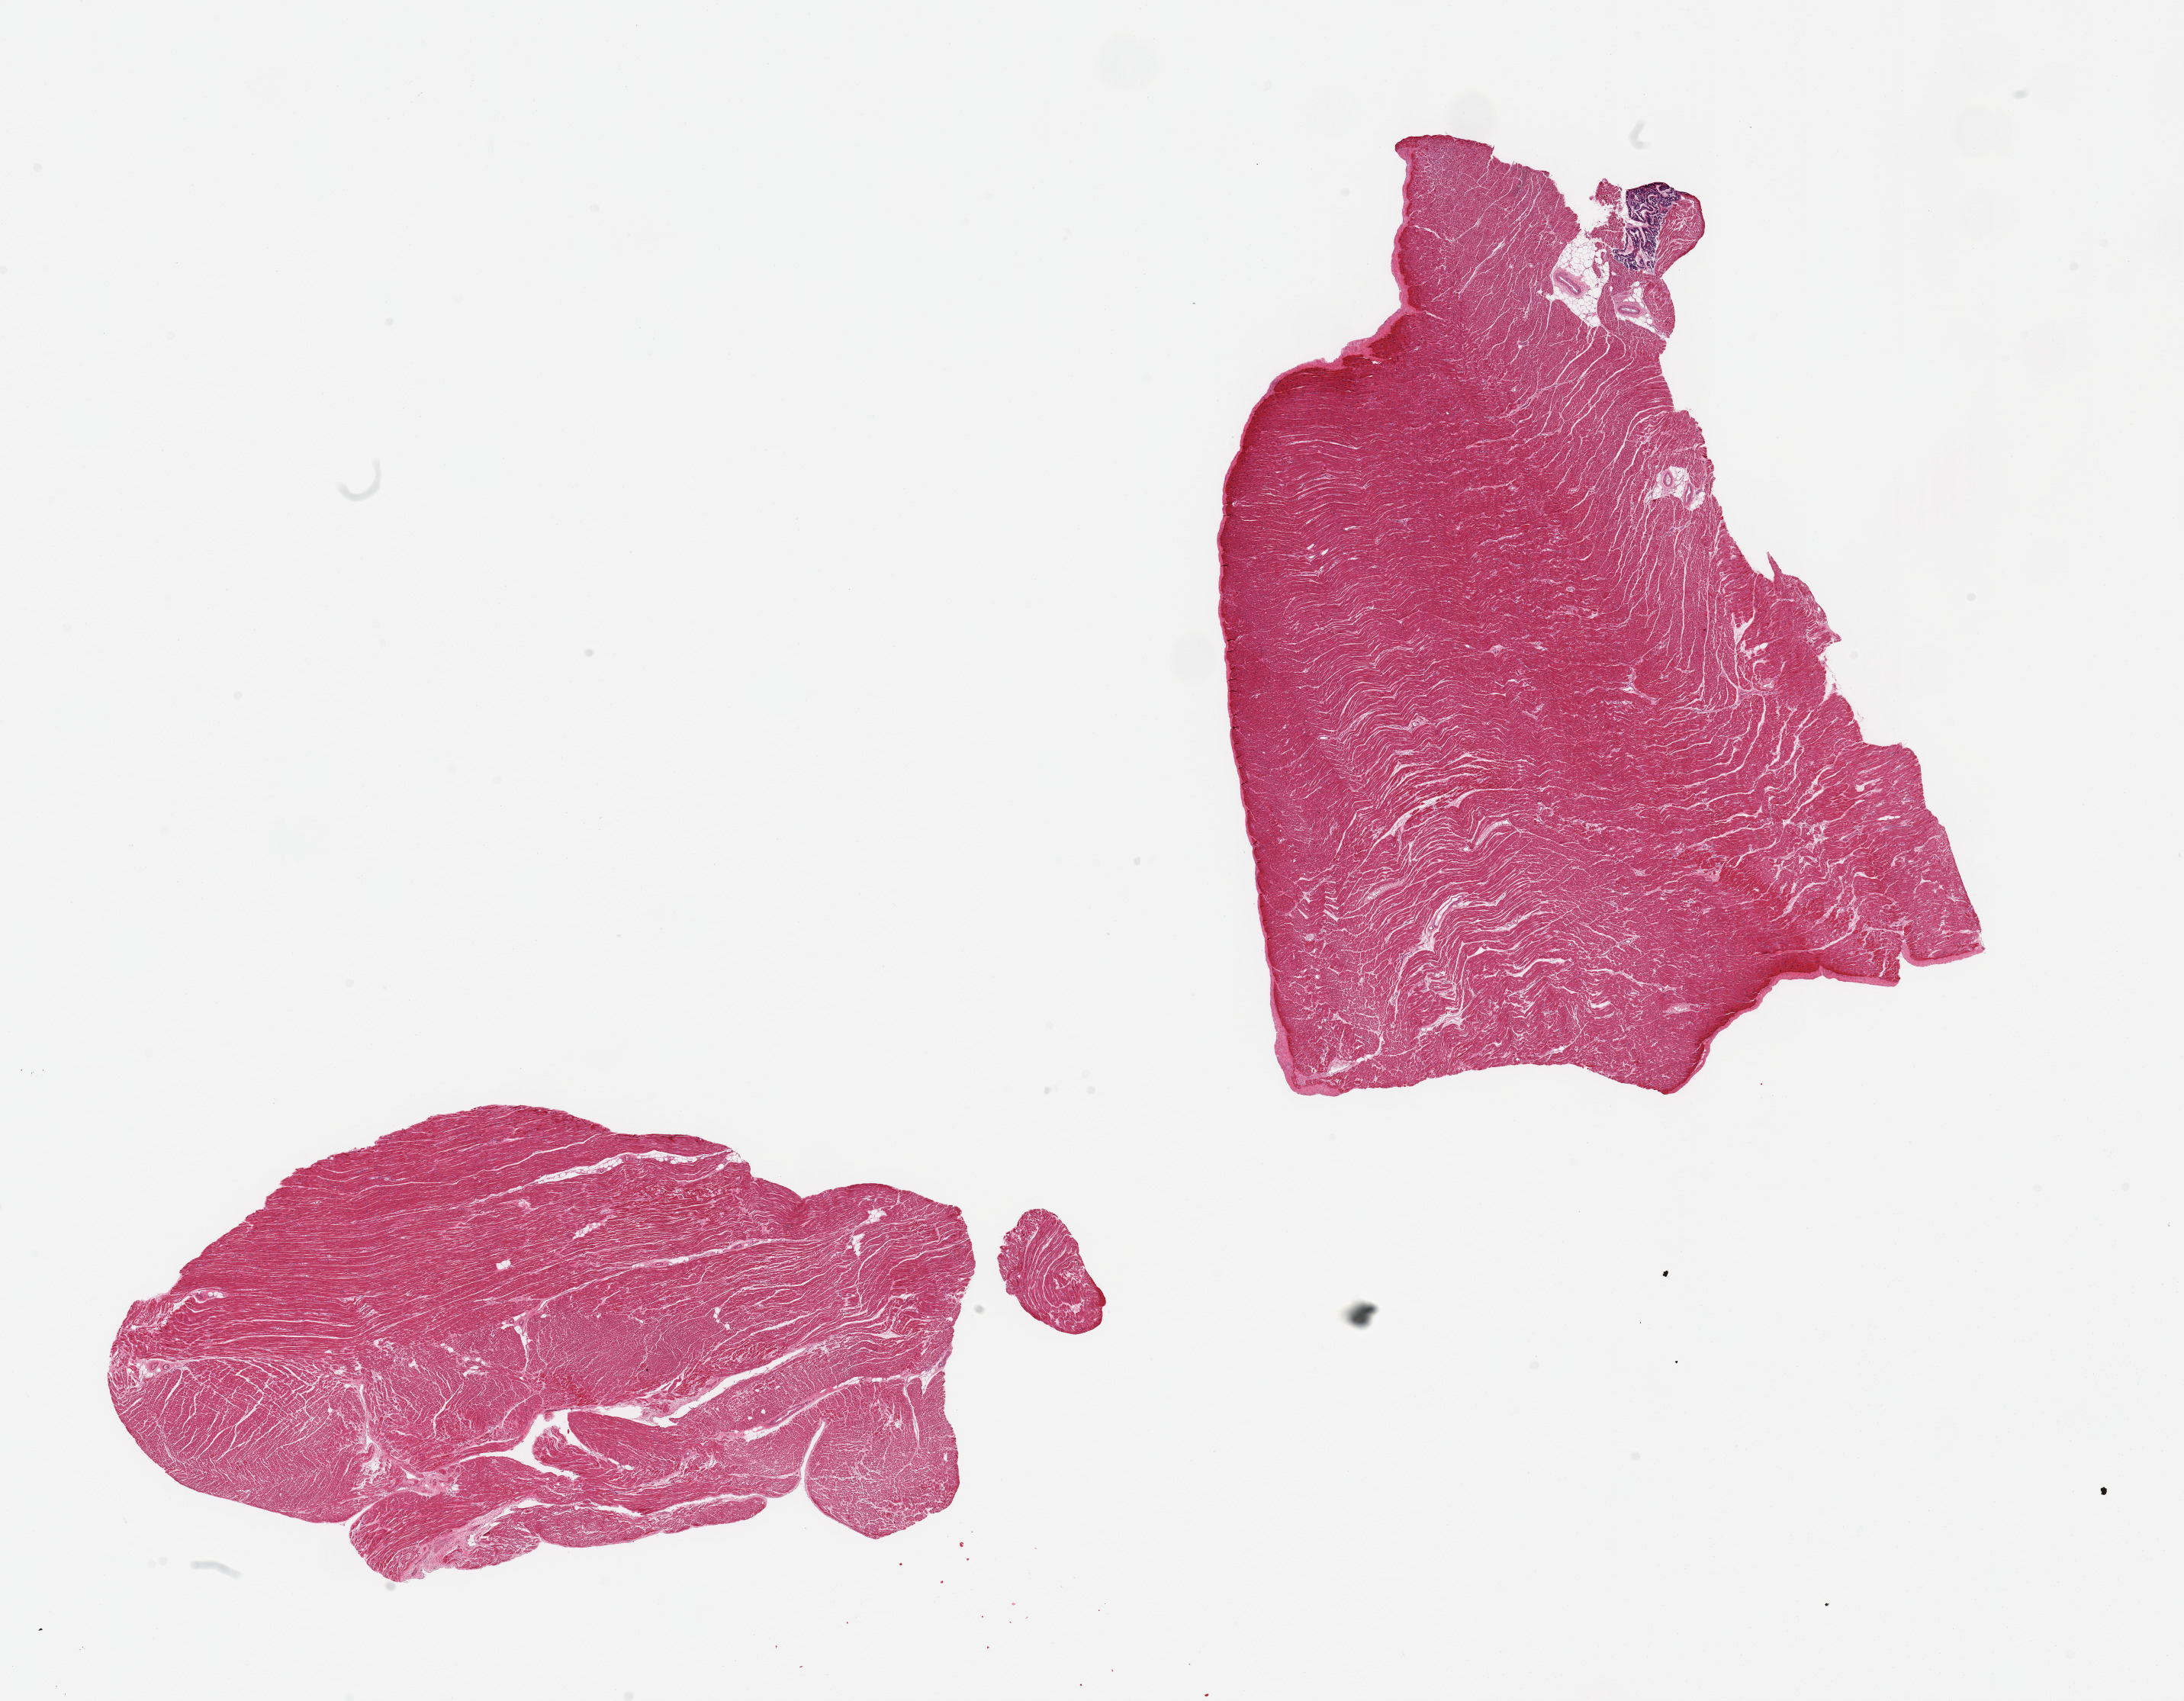
Digitized H&E-stained section, a low-resolution overview of the entire scanned area, about 22.6 x 17.6 mm; PAXgene-fixed, paraffin-embedded tissue; target tissue: auricular appendage; tissue donor sample. Donor sex: female.
Review note (as recorded): 2 pieces; ventricular myocardium, not atrium.